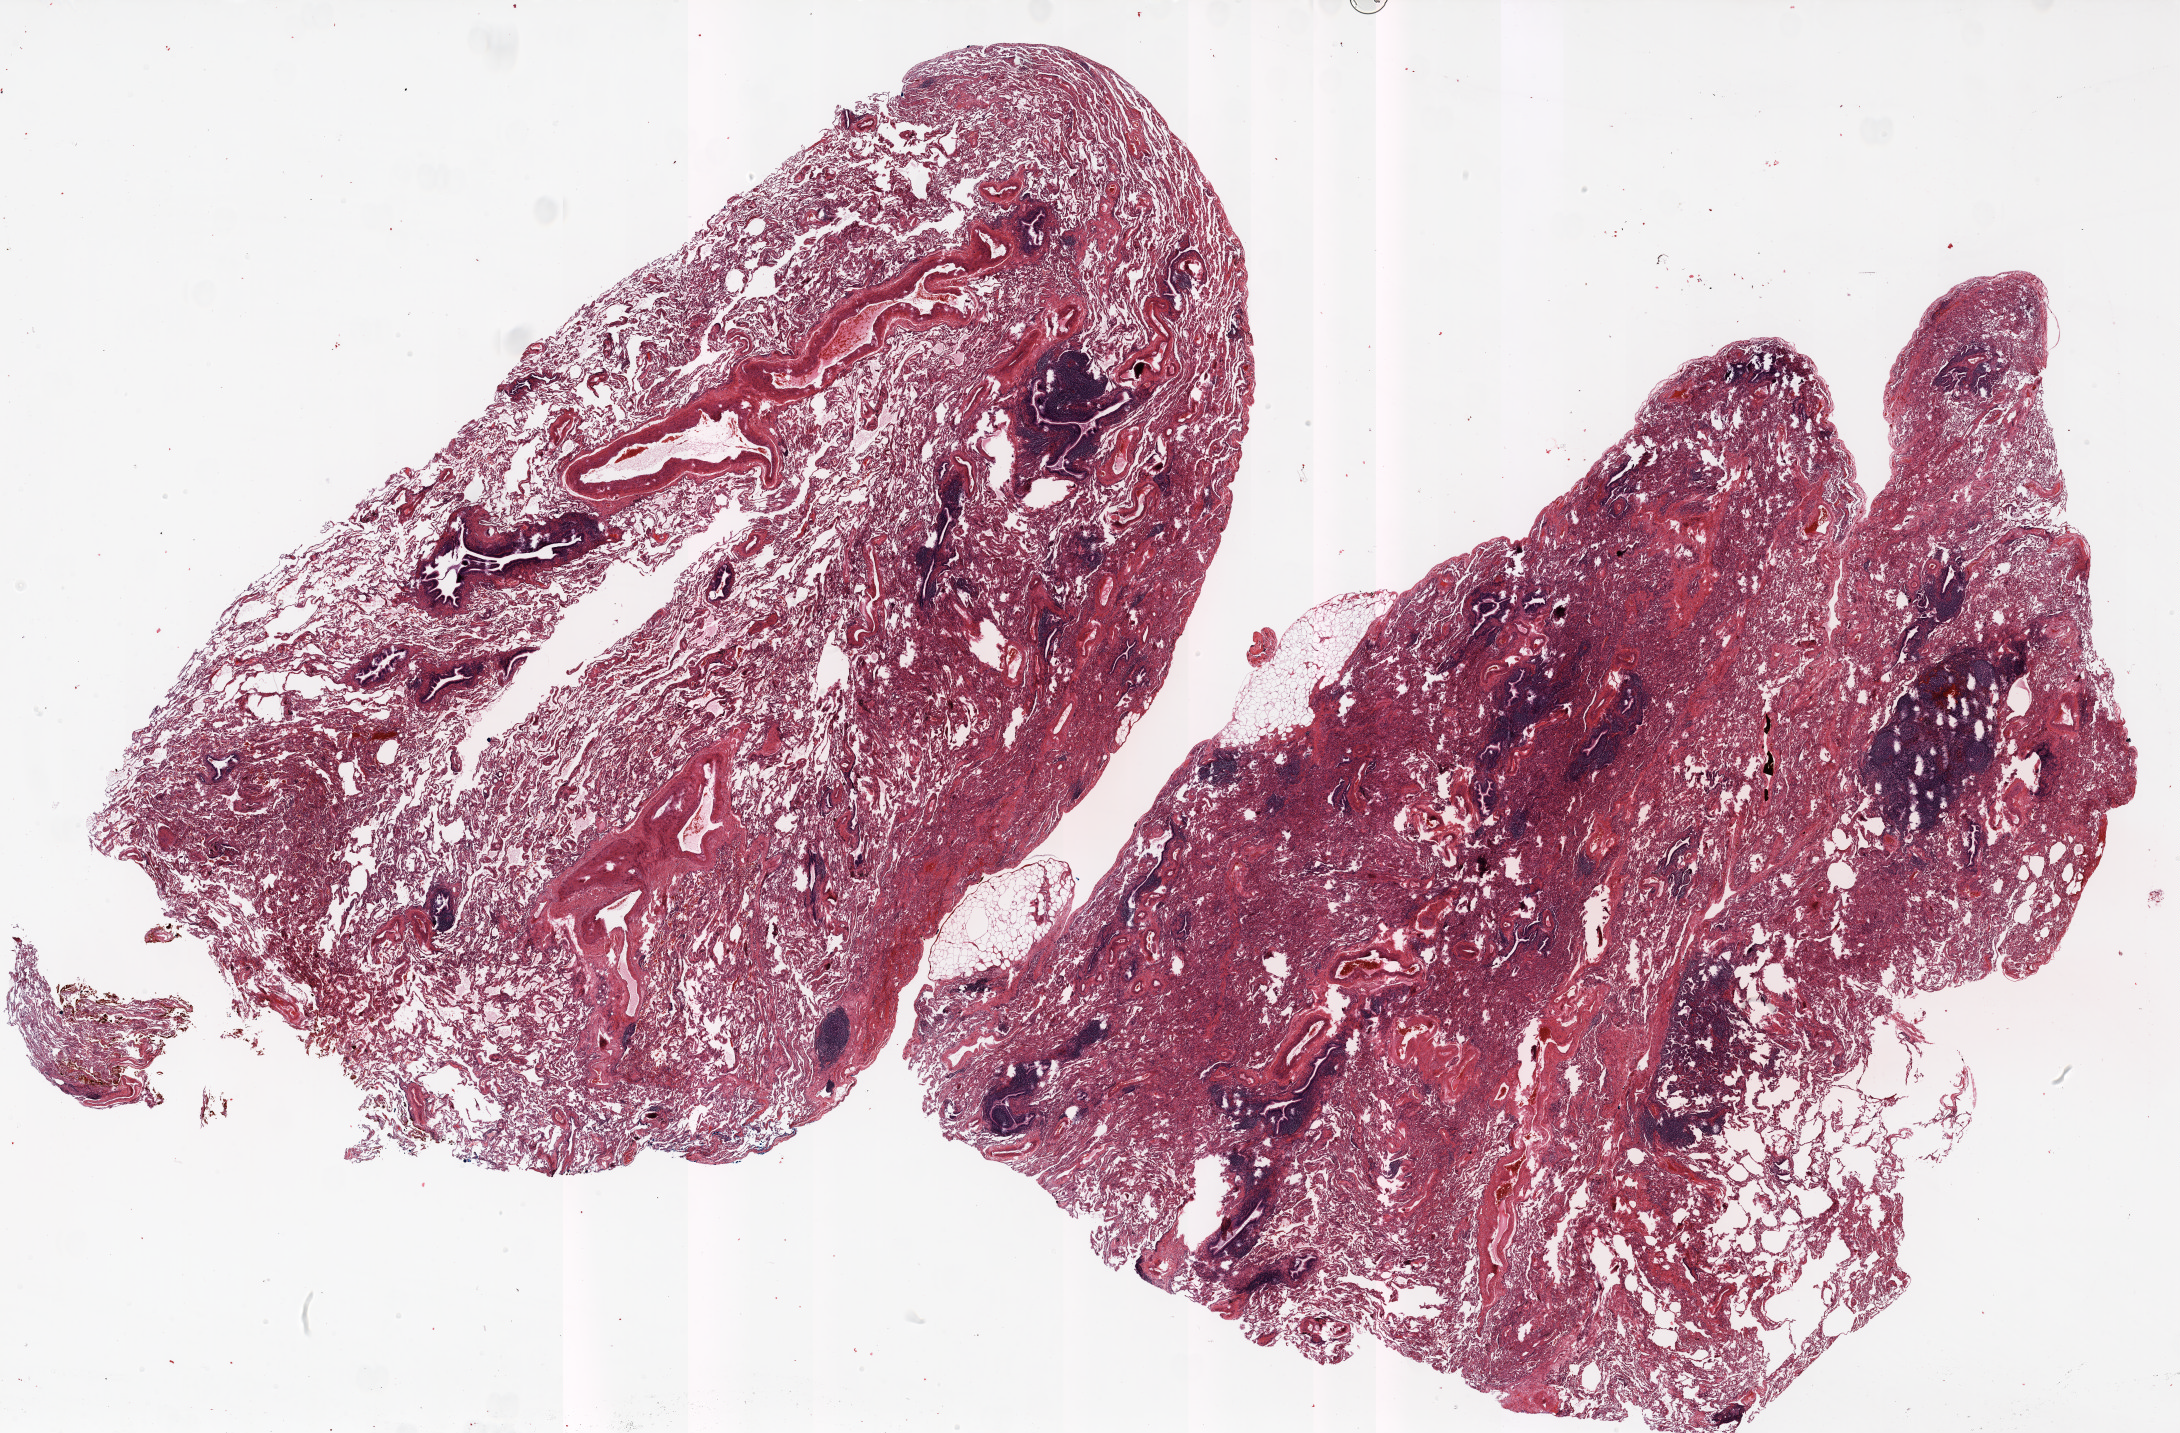
Whole-slide histology image, Hematoxylin and eosin (H&E) stained — shown as a low-resolution overview of the whole scanned area (about 35.0 x 23.0 mm, slide scanned at 20x), formalin-fixed paraffin-embedded (FFPE) section, lung. Female patient, aged 72 at enrolment. Former smoker at enrolment. Grade: moderately differentiated (G2).
- primary tumour location (clinical record): left upper lobe
- tumour size (pathology): 25 mm
- participant's lung-cancer diagnosis: Adenocarcinoma, NOS
- stage (AJCC 6th edition): IA
- ICD-O-3 topography: upper lobe of lung (C34.1)
- note: participant had 2 primary lung cancers recorded; fields above describe the first